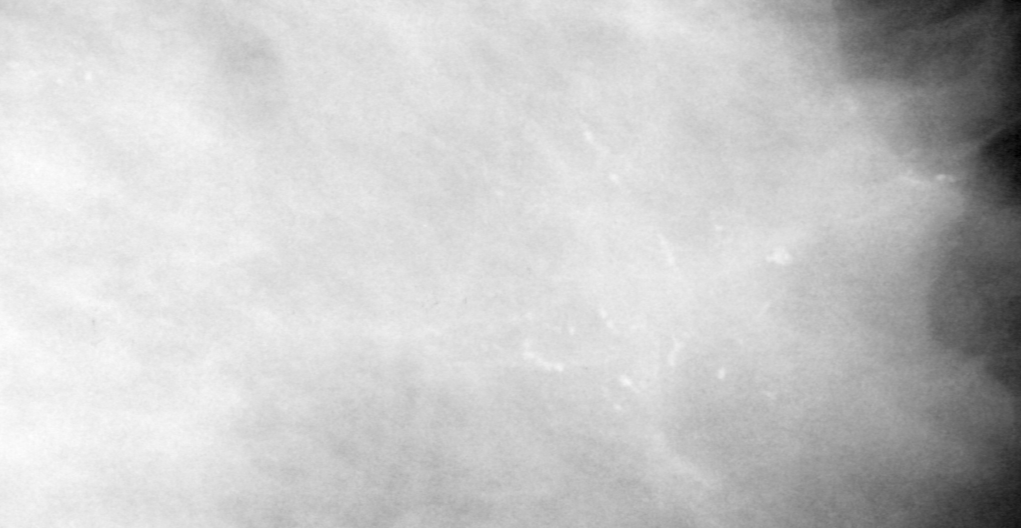
Cropped region of a digitized screen-film mammogram centred on a radiologist-marked abnormality; right breast; MLO view.
- Marked abnormality: calcifications, morphology pleomorphic, distribution segmental; BI-RADS assessment category 5; pathology (as recorded): malignant.